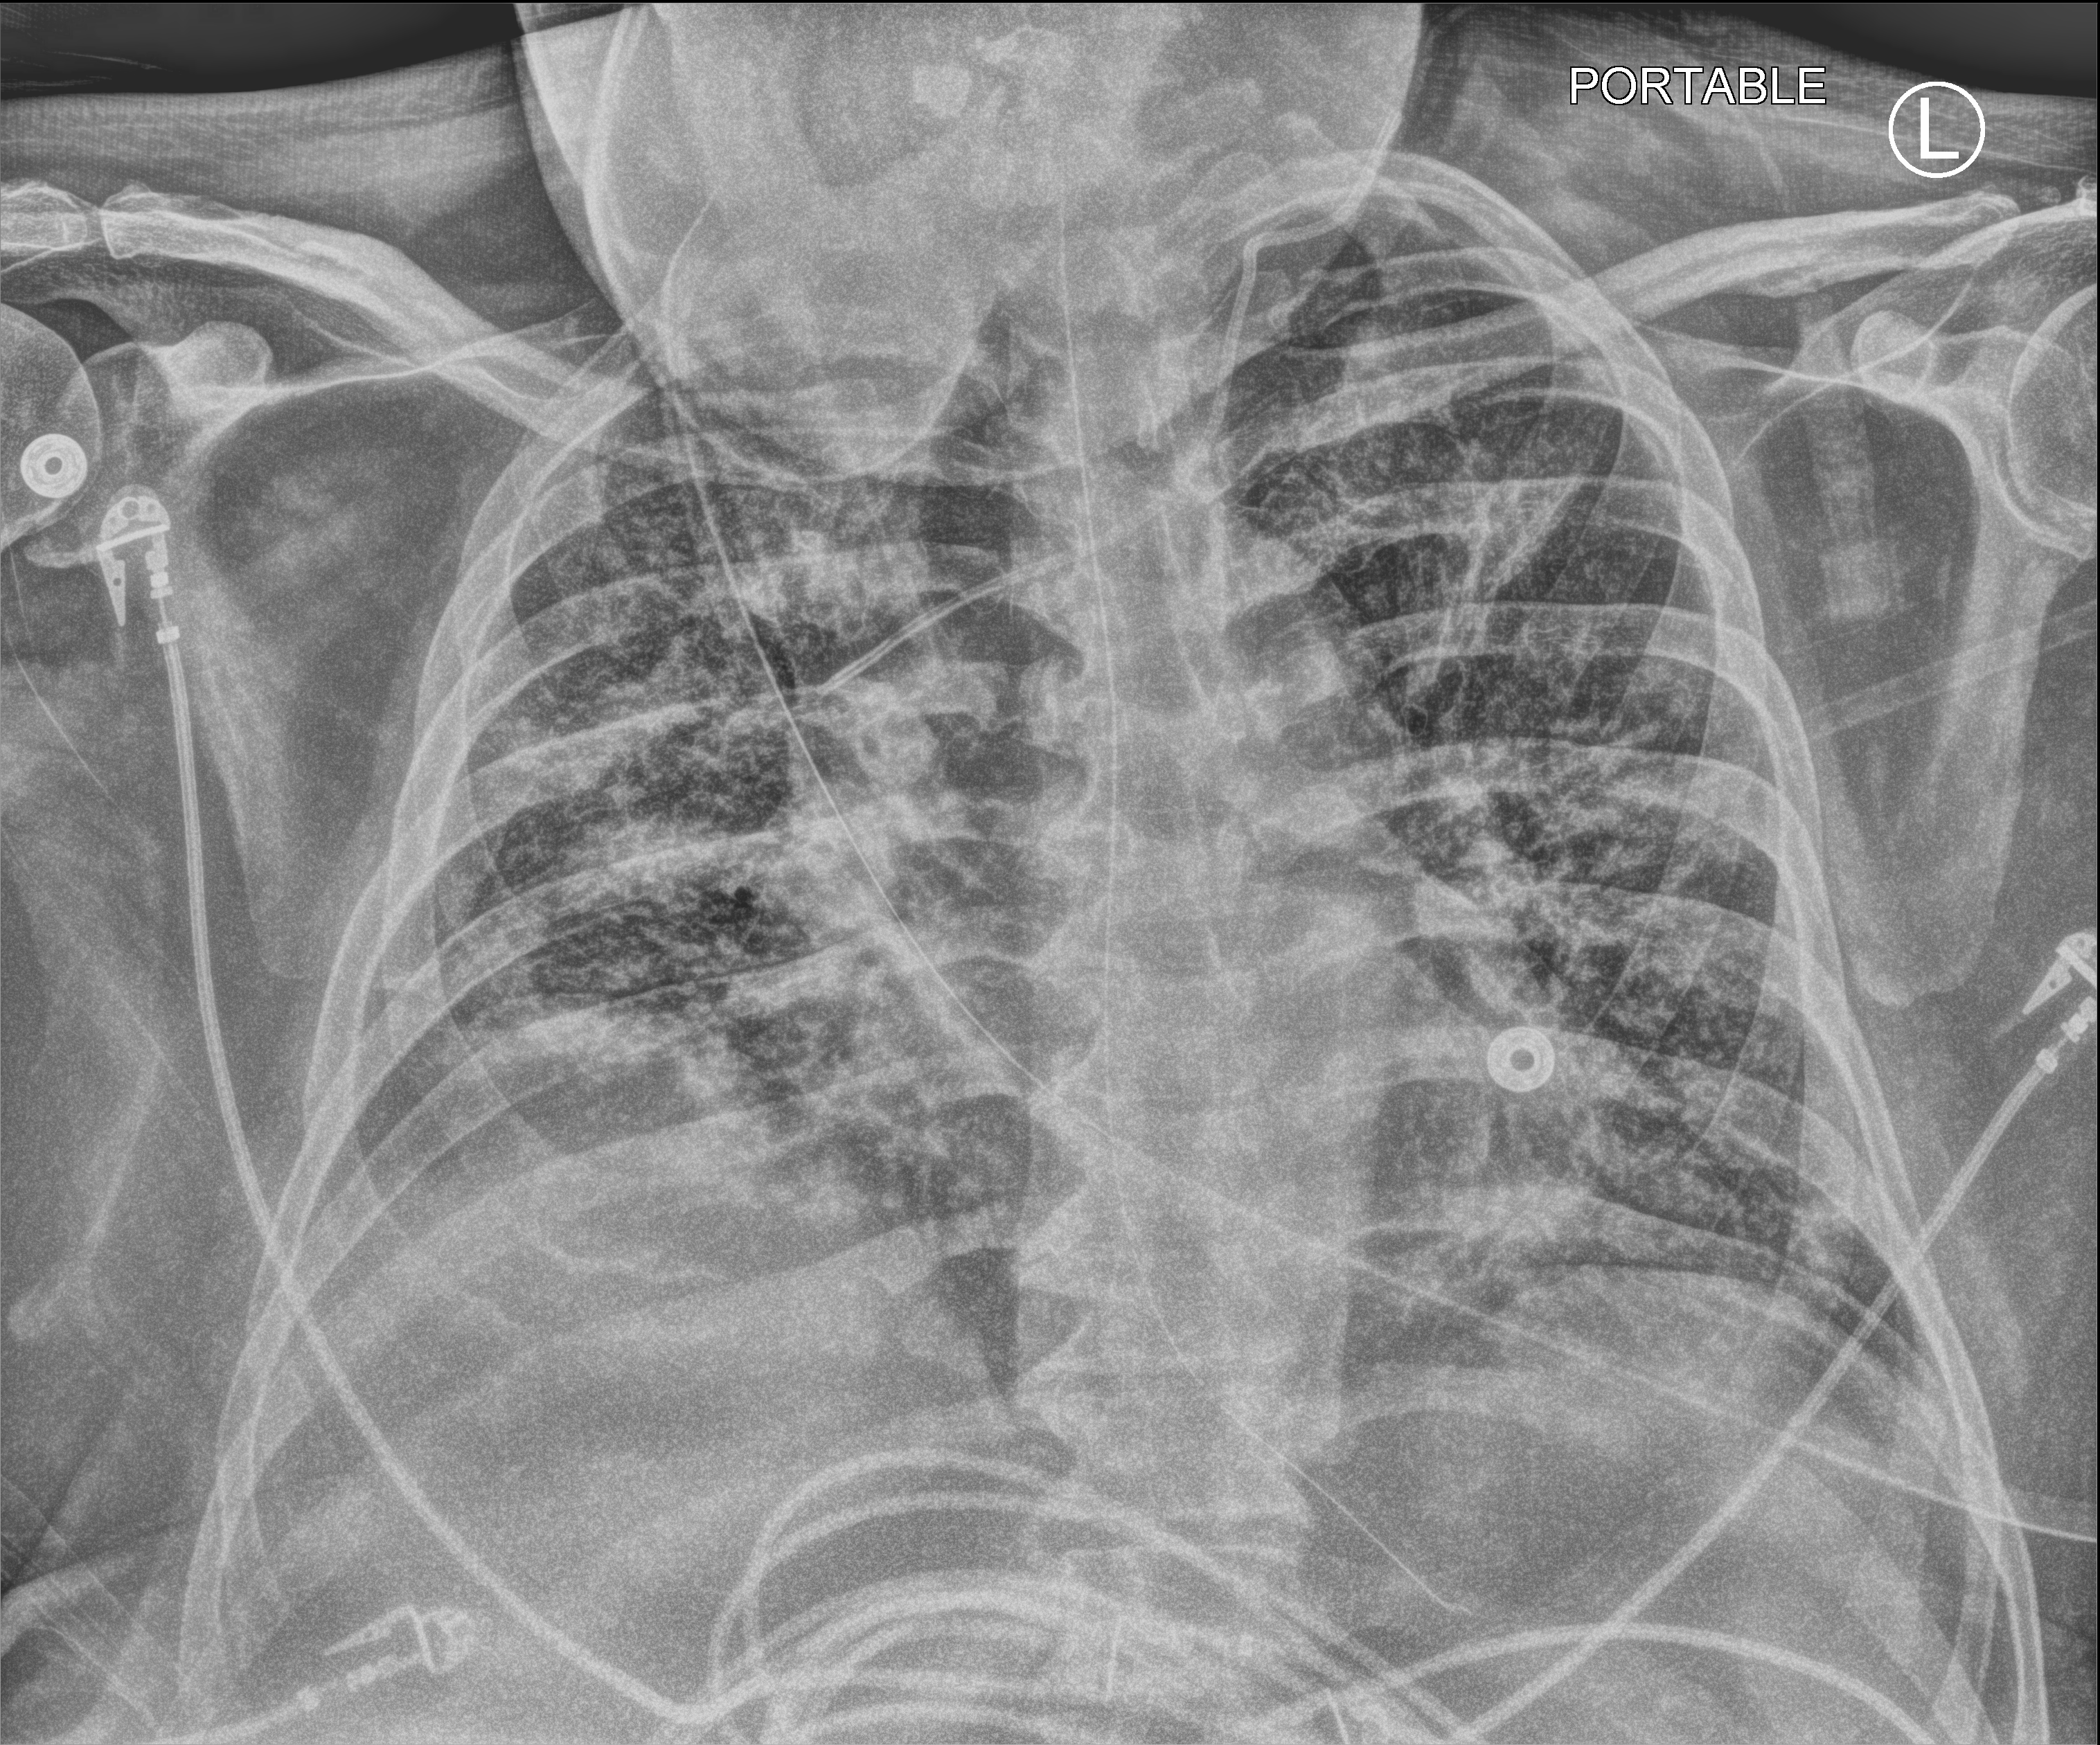
Chest X-ray (portable); anteroposterior (AP) projection. Male patient hospitalised with COVID-19, age 18–59 years.
Admission-level facts for this patient (not findings on this image; timing relative to this image not recorded): admitted to intensive care during this hospital stay: yes; mechanically ventilated during this hospital stay: yes.